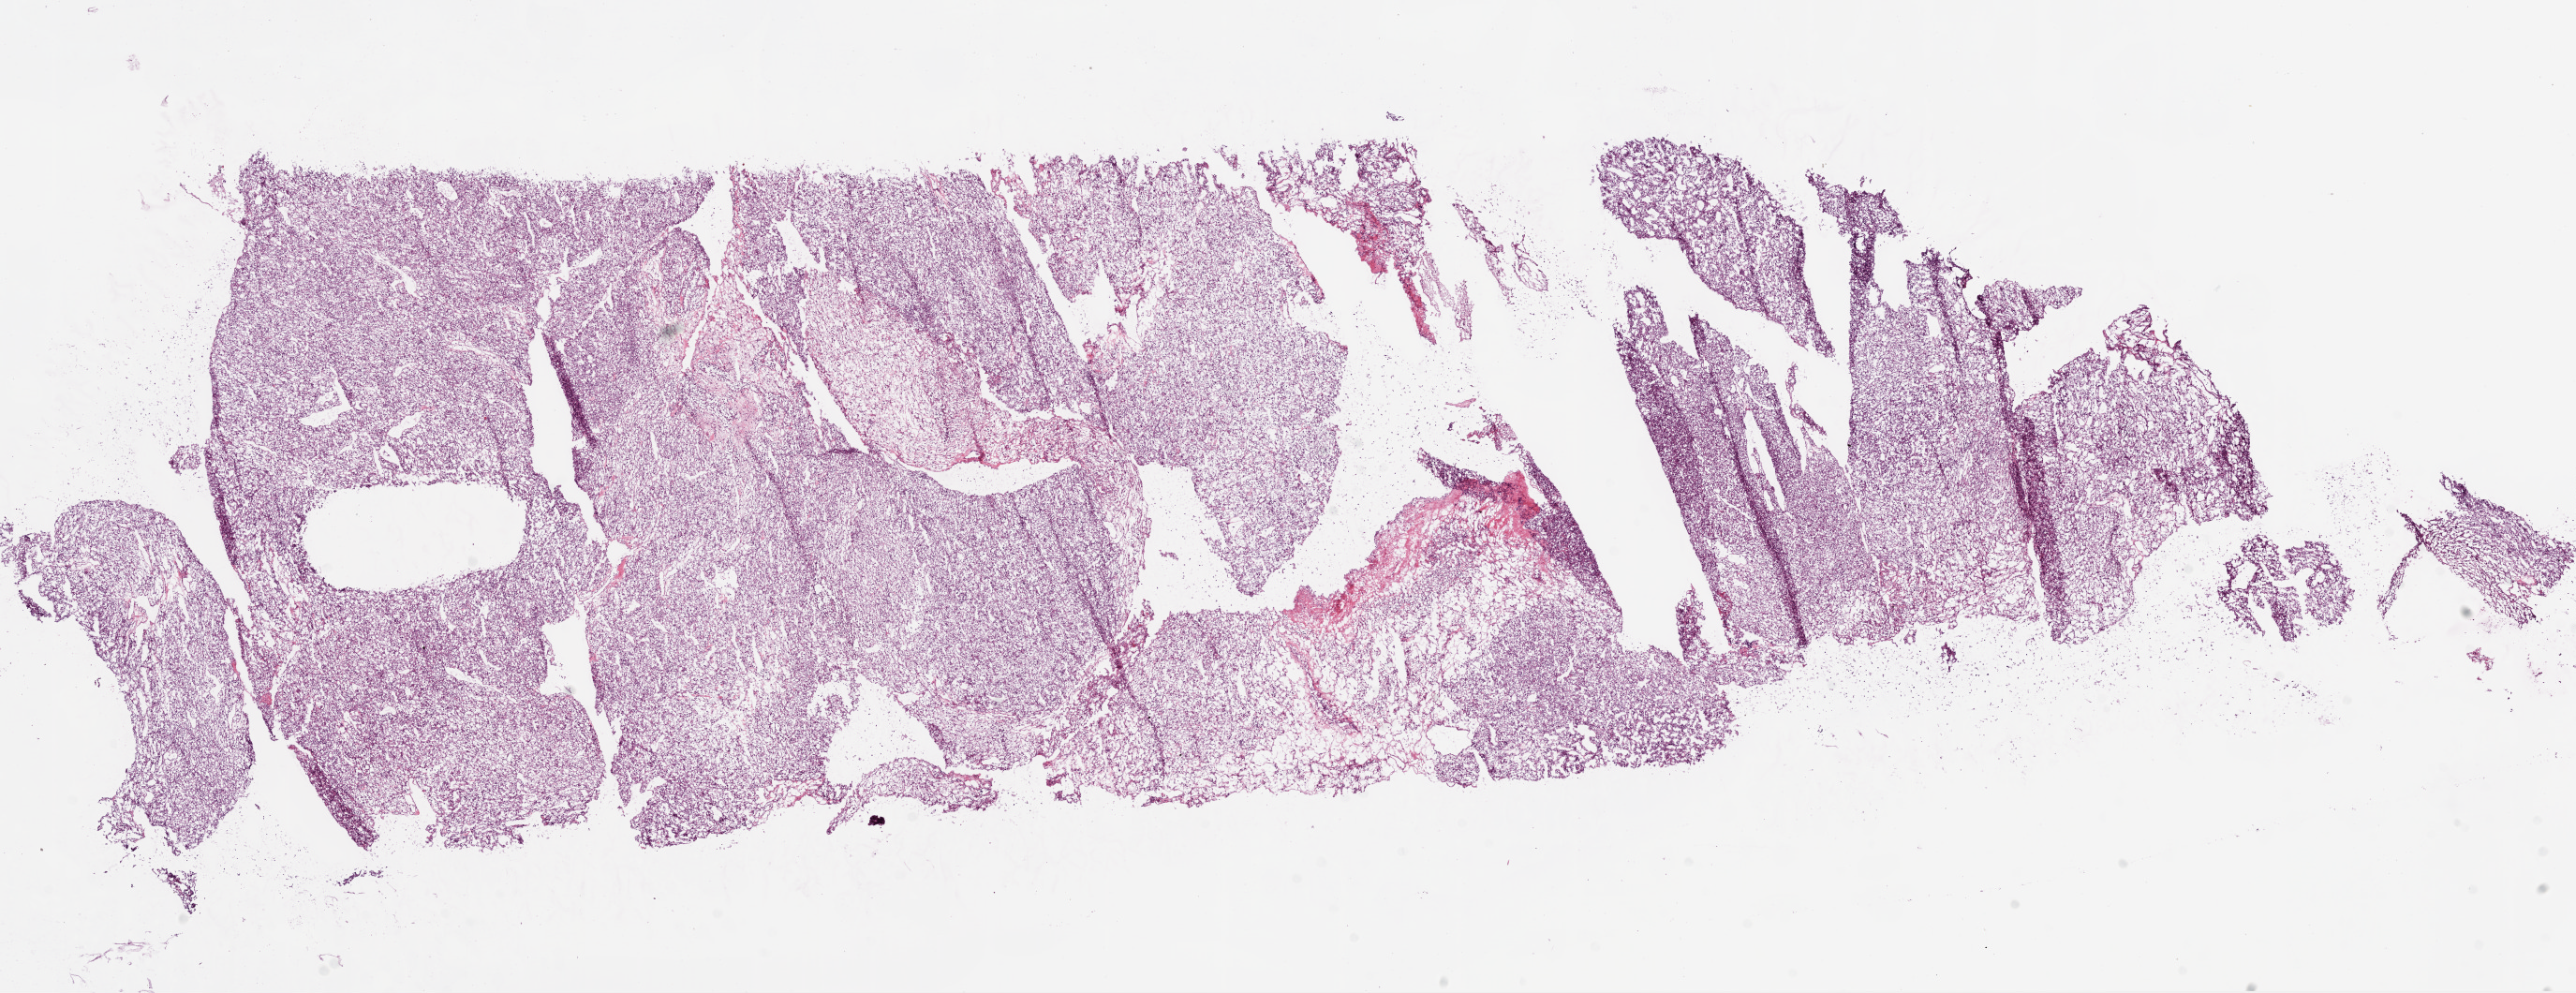
Hematoxylin and eosin (H&E) stained whole-slide image — low-resolution overview of the scanned area, about 22.1 x 8.5 mm (slide scanned at 20x). Frozen section from the bottom of the tissue portion. Sample: primary tumour, kidney. Patient: female, age at initial diagnosis 73 years. Histologic grade: G3 (poorly differentiated). Pathologist review of this section (percent, as recorded): tumour cells 95%, tumour nuclei 90%, normal cells 0%, stromal cells 5%, necrosis 0%.
Laterality: left. Histologic diagnosis: Clear cell adenocarcinoma, NOS. TNM: T1b N0 M0. AJCC pathologic stage: I.